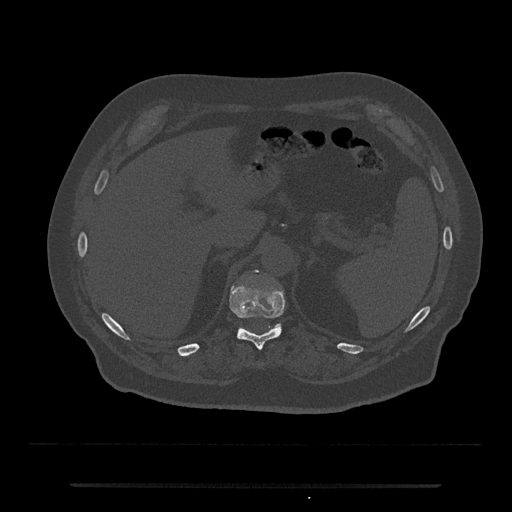
CT including the spine, one axial slice. Slice 641 of 797 in the series (ordered by position). Bone window (W 1800 / L 400 HU). 512 × 512 image matrix, field of view 434 × 434 mm. Male patient, age 80 years. Case-level facts recorded for this patient, not image findings: primary cancer: prostate; vertebrae with lytic lesions (as recorded): L1, T11.
Annotated regions visible in this slice (semi-automatic segmentation, software-assisted and operator-edited):
- T11 vertebra: box from (x=230, y=287) to (x=284, y=350) px
- T12 vertebra: (x=239, y=269)–(x=282, y=330)